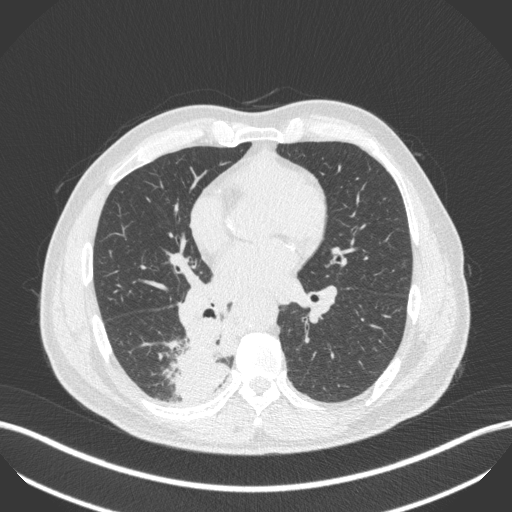
Chest CT, one axial slice. 100 kVp. Lung window (W 1500 / L -600 HU). 1 mm slice thickness. 512 × 512 image matrix, field of view 400 × 400 mm. Patient: male, 61 years. From the clinical record (not read from this slice): clinical TNM (as recorded): T1 N0 M0.
Annotated regions visible in this slice (rectangle marked by the reading radiologist):
- lung tumour (recorded histology: small cell carcinoma): bounding box (x1, y1, x2, y2) in pixels: (166, 316, 233, 397)